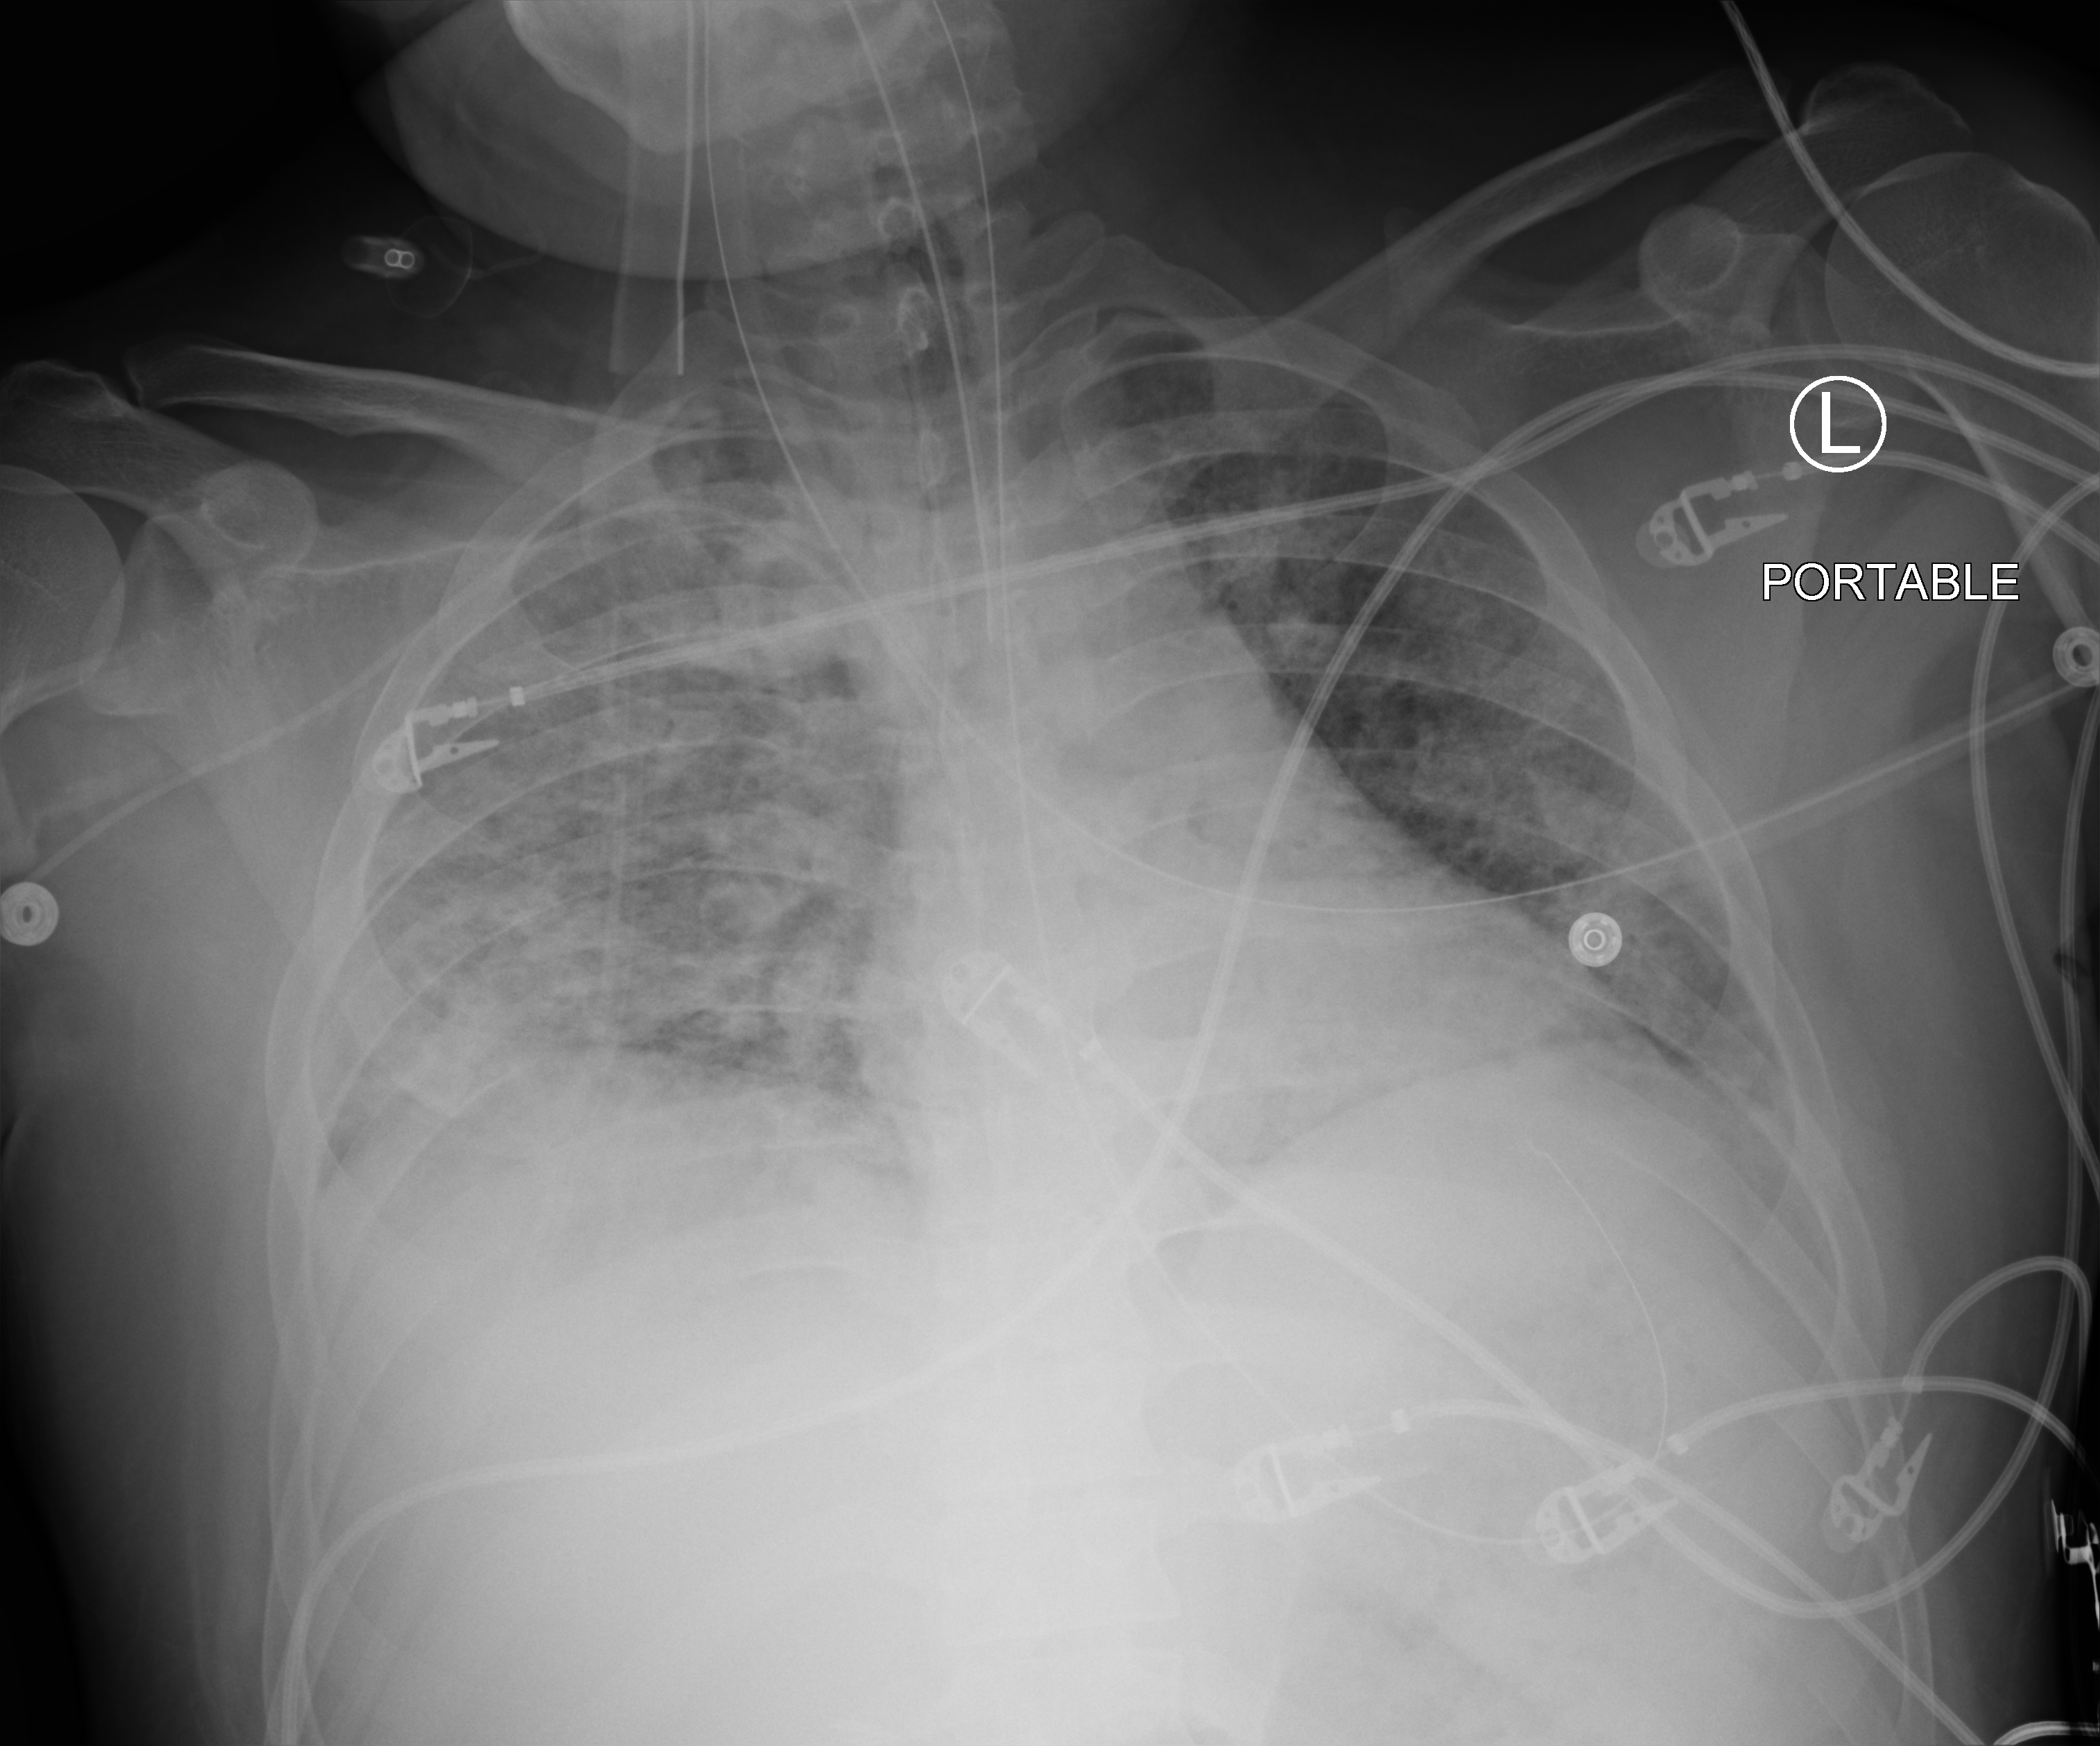
Bedside chest radiograph (computed radiography); anteroposterior (AP) projection. Patient hospitalised with COVID-19; male, aged 18–59 years.
Admission-level facts for this patient (not findings on this image; timing relative to this image not recorded): COPD (admission record): no; hypertension (admission record): no.